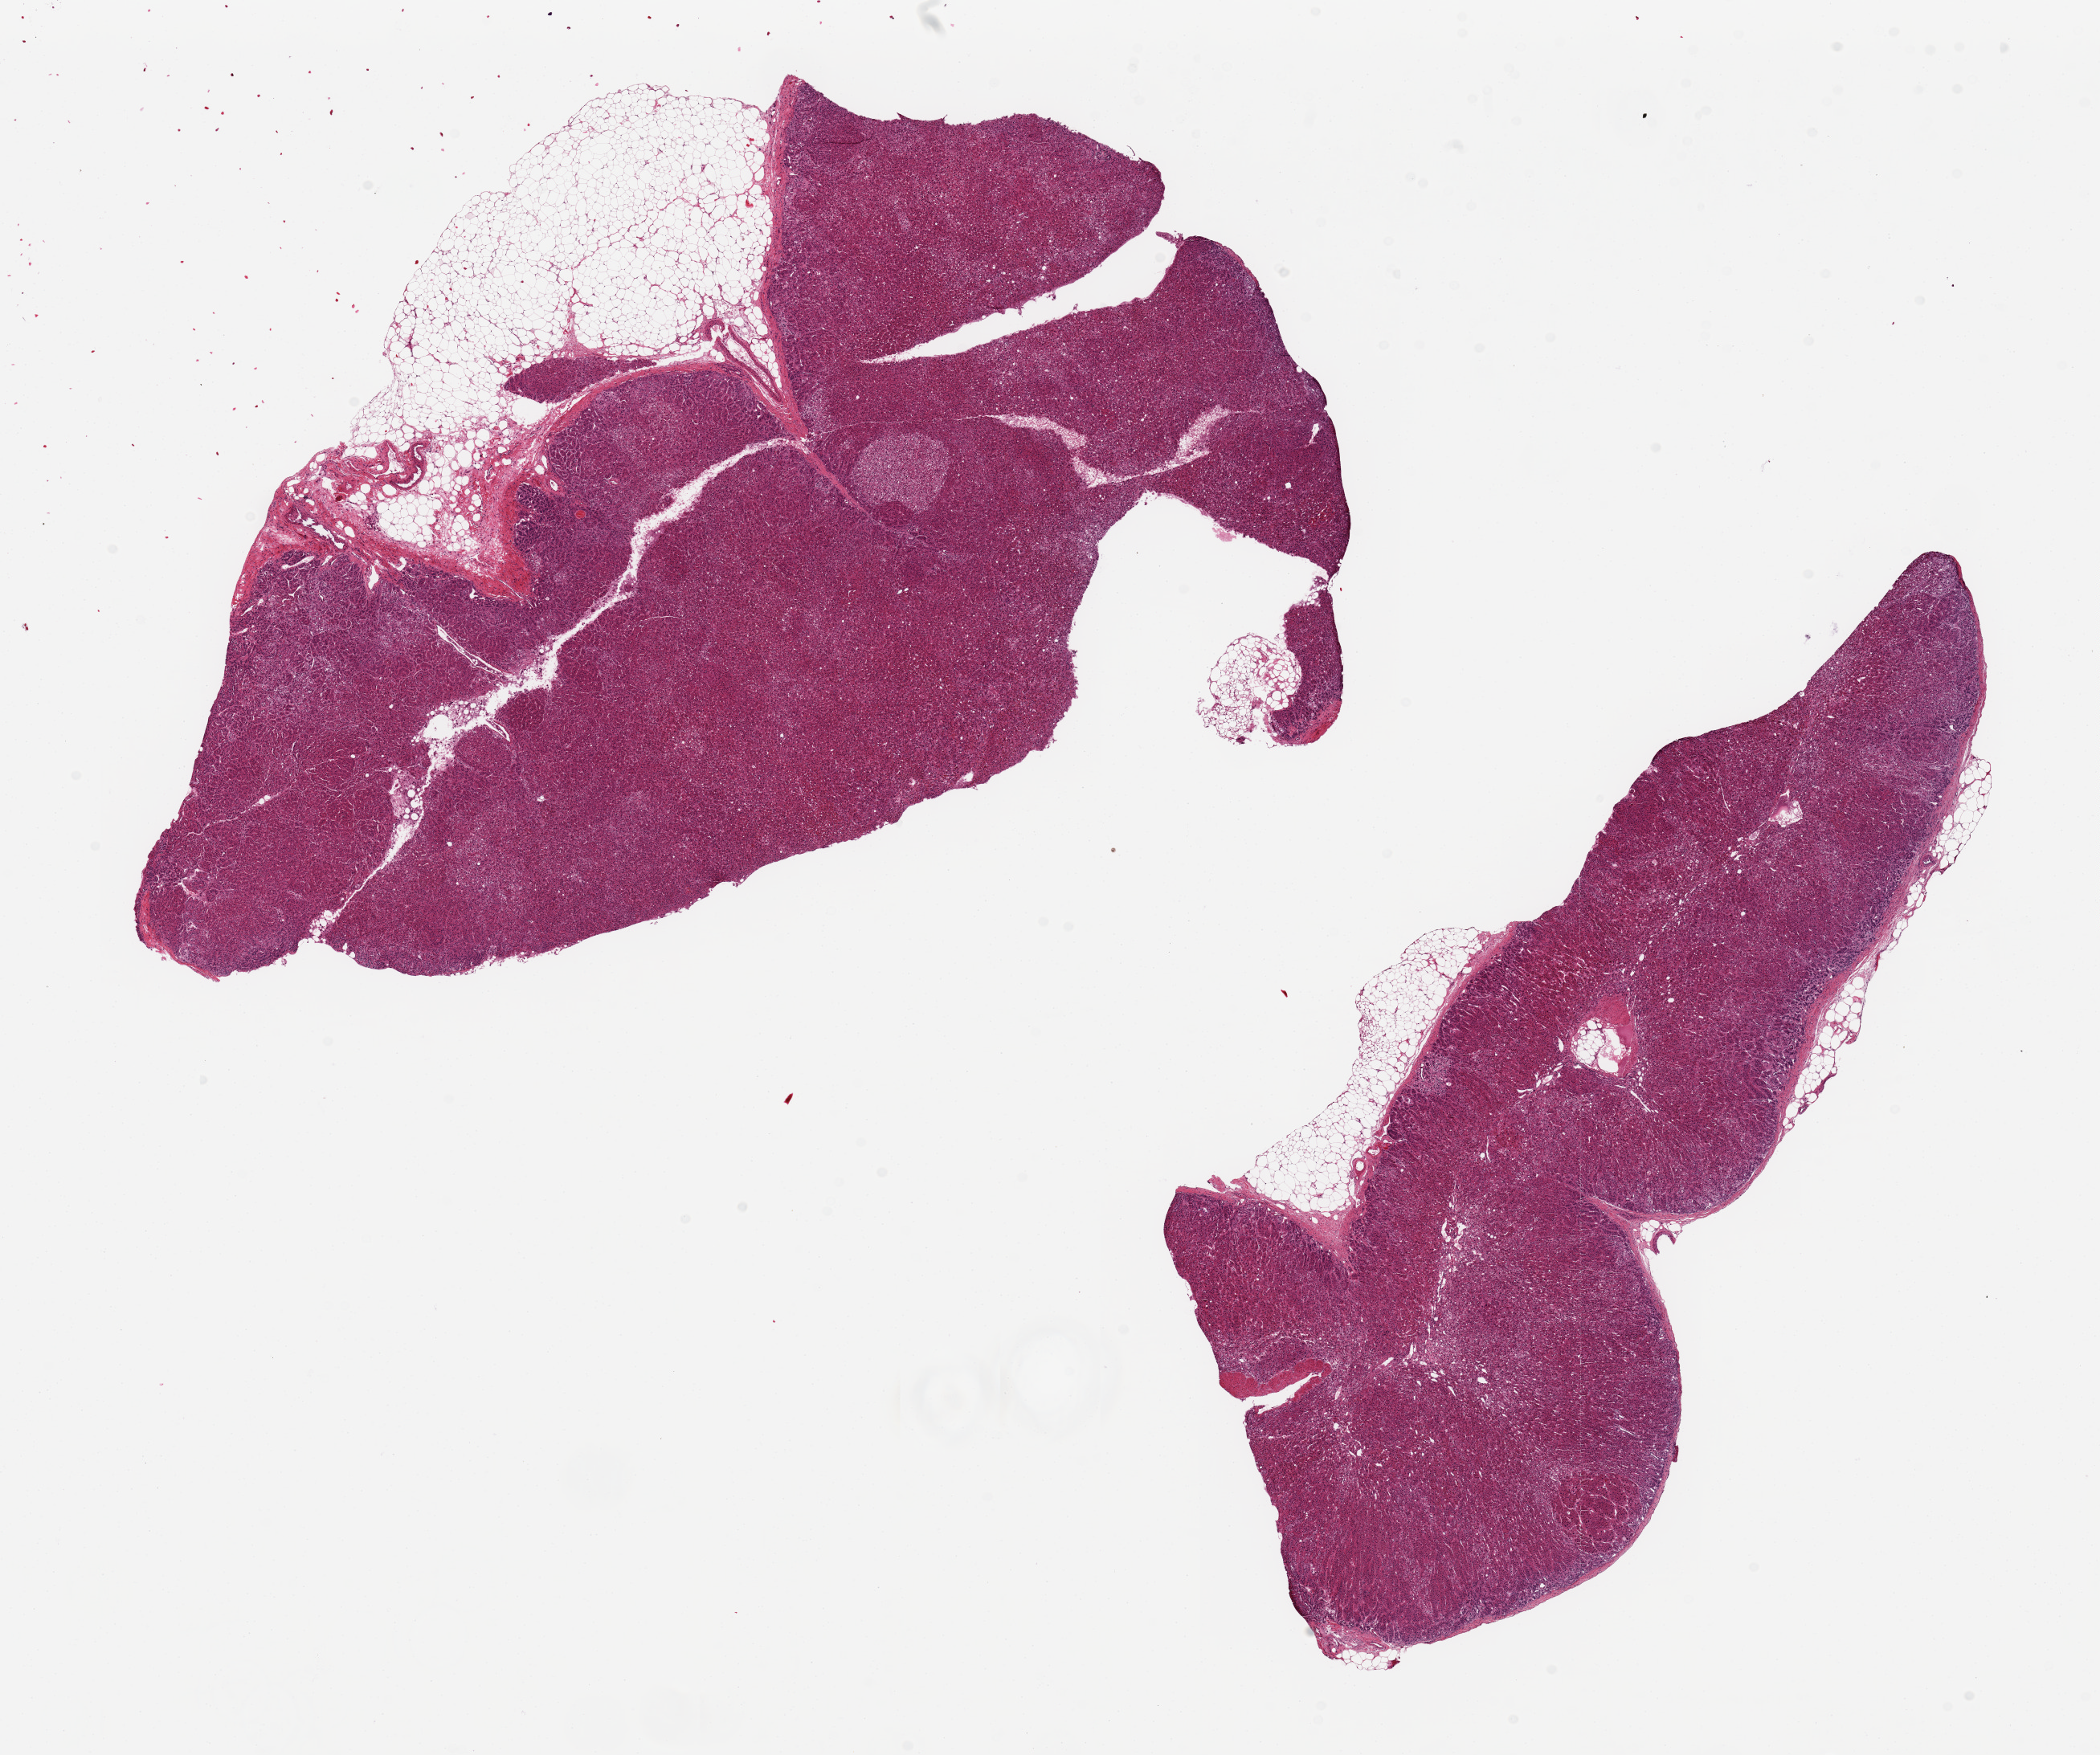
Digitized haematoxylin and eosin-stained section — low-resolution overview of the scanned area, about 20.7 x 17.3 mm (from a 20x scan); PAXgene-fixed paraffin-embedded (PFPE) section; section of adrenal gland (target tissue); donor tissue sample.
Reviewer comment on this tissue sample: 2 aliquots, ~11x6mm.